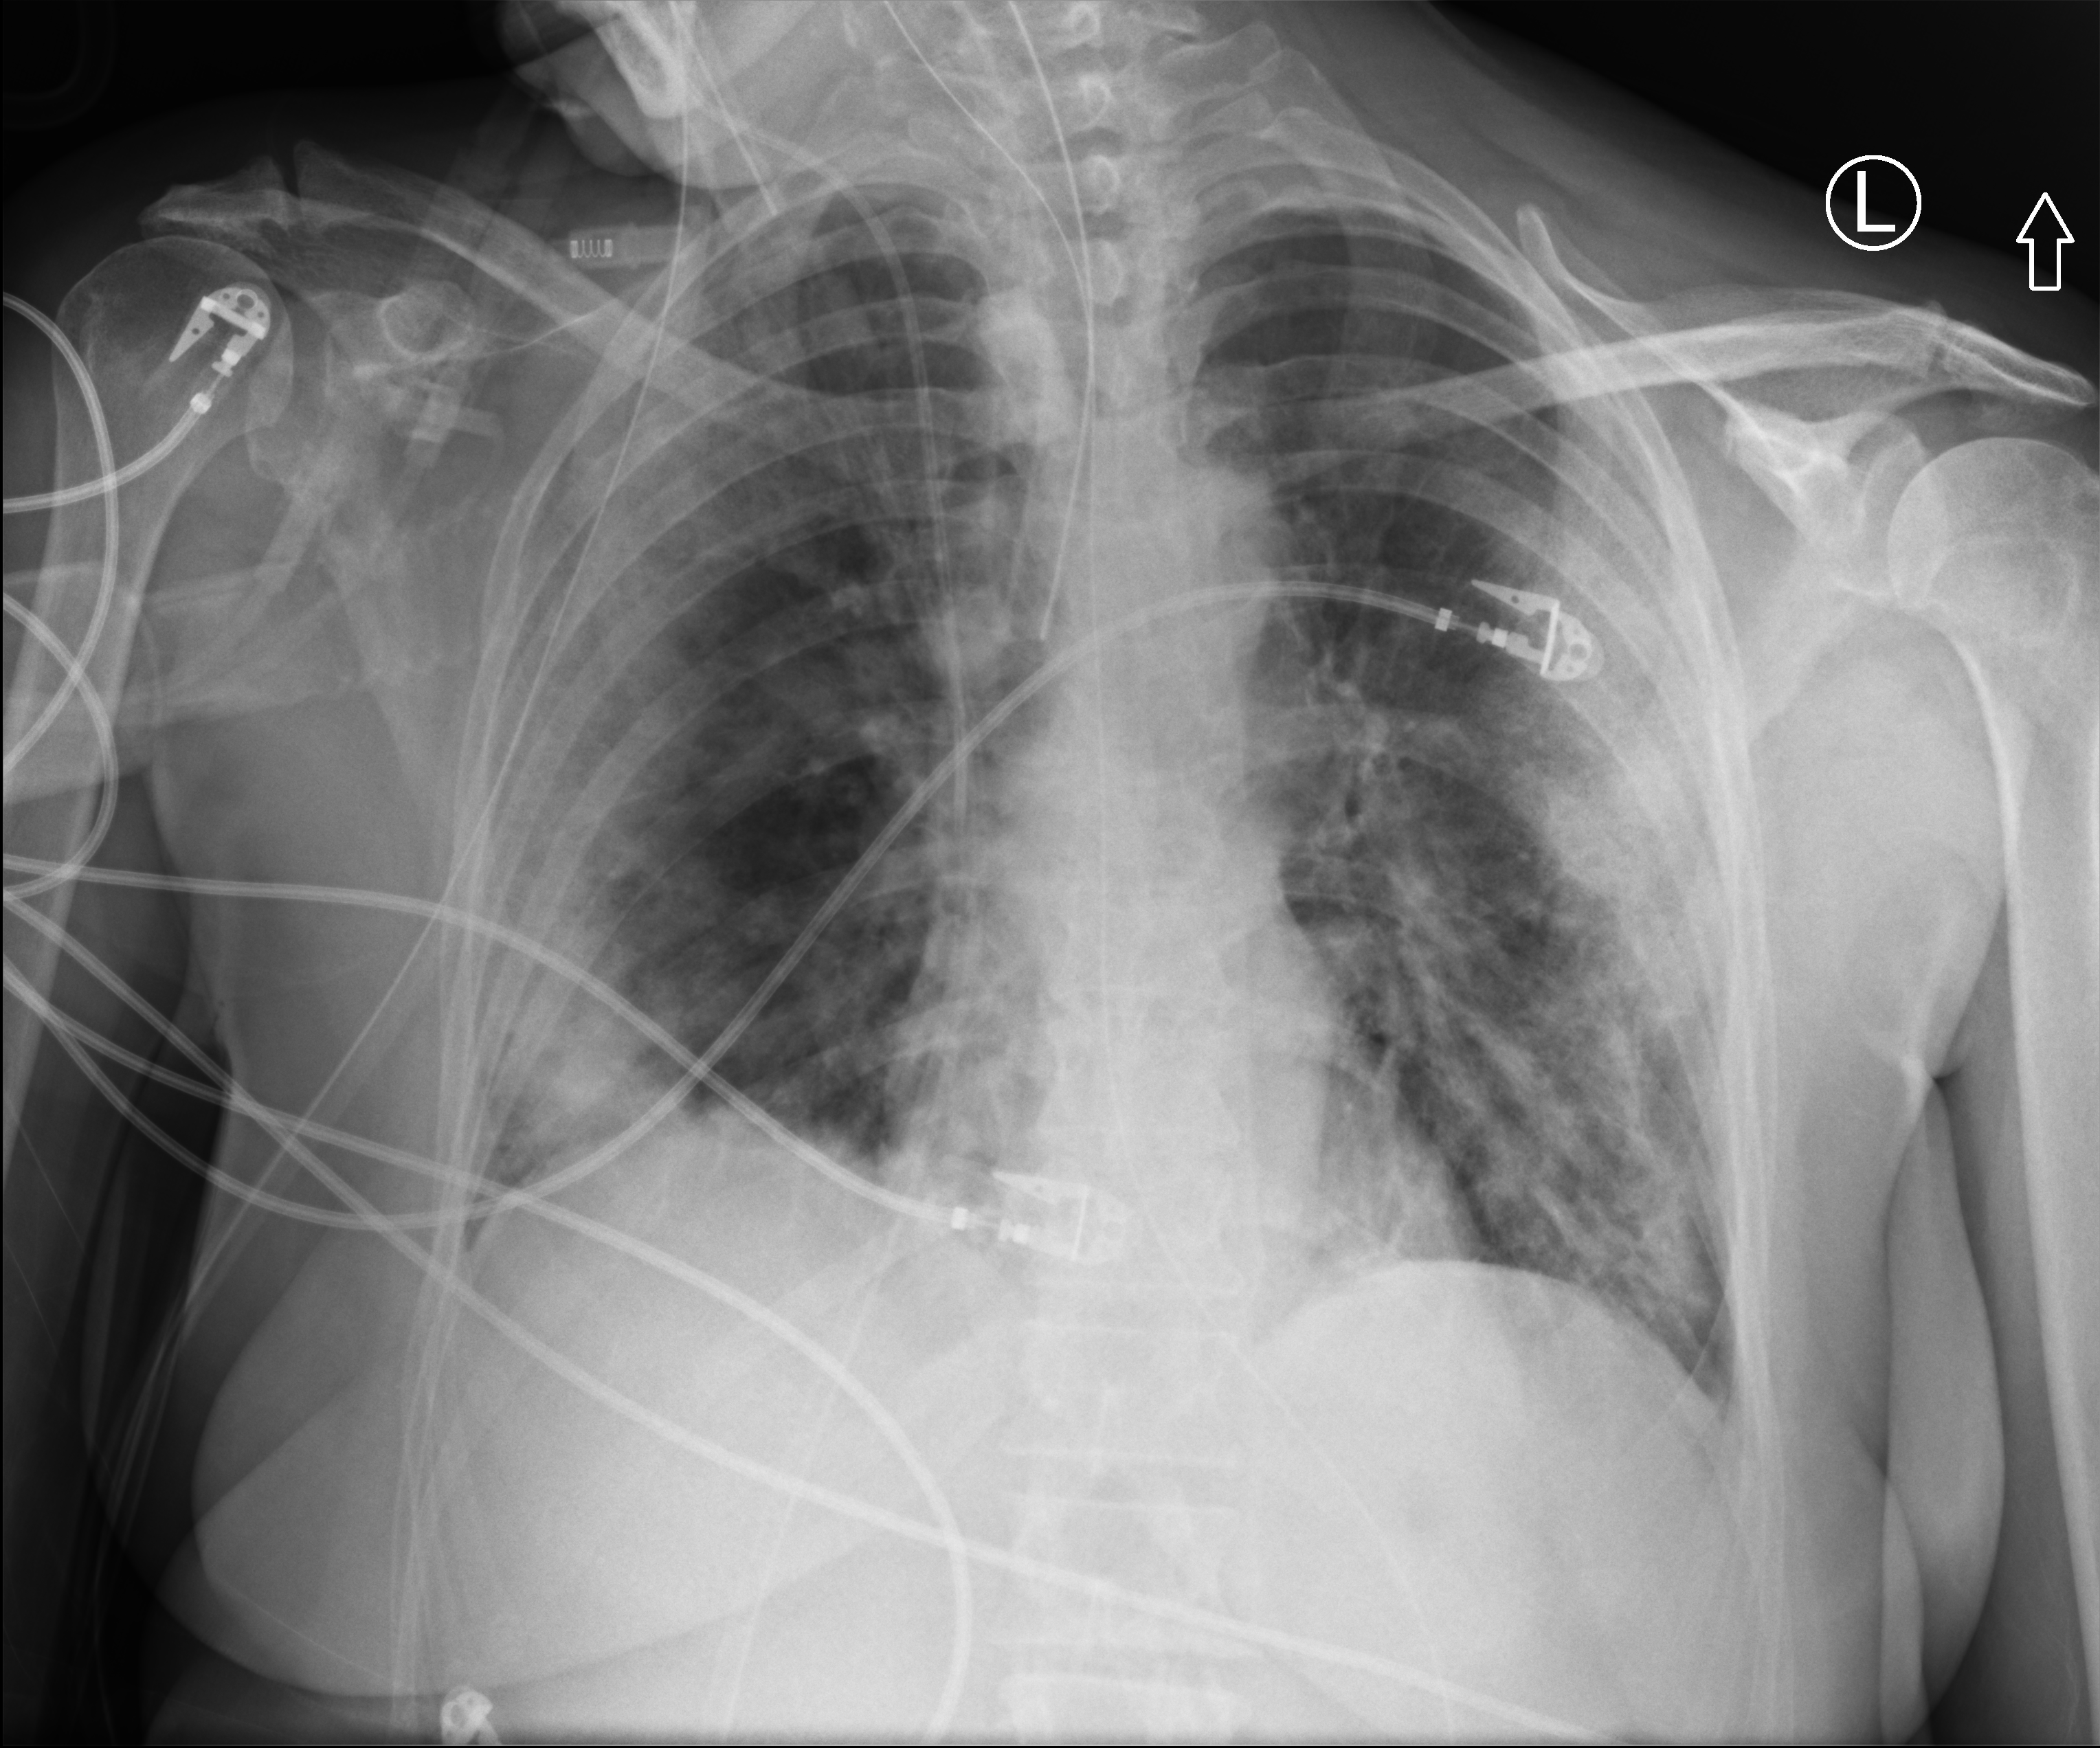
Chest X-ray (portable), anteroposterior (AP) projection. Female patient hospitalised with COVID-19, age 60–74 years.
Admission-level facts for this patient (not findings on this image; timing relative to this image not recorded): admitted to intensive care during this hospital stay: yes.